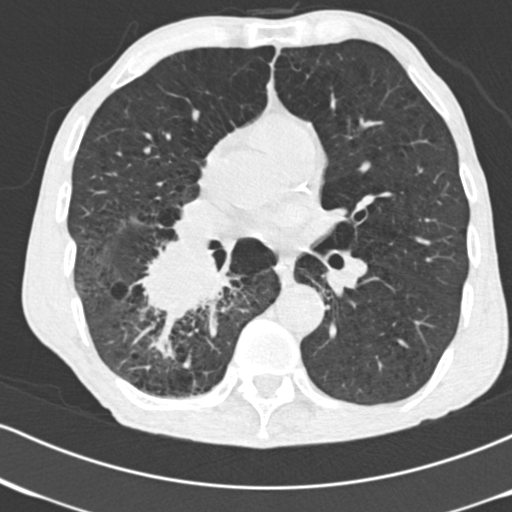
Low-dose screening chest CT, axial slice, second annual screen, lung window (W 1500 / L -600 HU), 2 mm slice thickness, standard (soft-tissue) reconstruction kernel (B30f), slice 98 of 182 in the series. Male participant, aged 64 years at enrolment.
Expert-annotated lung lesion, bounding box <128,227,241,333> (left, top, right, bottom; pixels). The exam's reader record, not a measurement of the box and not confirmed to be the same lesion: non-calcified nodule or mass ≥4 mm, 52 × 37 mm, spiculated (stellate) margins, soft tissue attenuation, pre-existing on the prior screen: no.